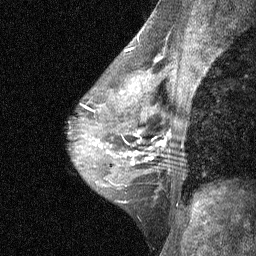
Breast MRI (dynamic contrast-enhanced), one sagittal slice. Slice 39 of 64 in the series (ordered by position). Dynamic contrast-enhanced study with each time point stored as its own series, time point 3 of 4 at this slice position (ordered by acquisition time). 1.5 T. TE 4.8 ms, TR 27 ms. 2 mm slice thickness. 256 × 256 image matrix, field of view 180 × 180 mm. Female patient, age 44 years. From the clinical record (not read from this slice): setting: breast cancer imaged before/during neoadjuvant chemotherapy; receptor status: HR-positive, HER2-negative.
Outlined on this slice (semi-automatic segmentation, software-assisted and operator-edited):
- analysis volume of interest (the breast-tissue region the enhancement analysis was run in; not a lesion): bounding box (x1, y1, x2, y2) in pixels: (115, 117, 185, 188)
- tumour enhancement mask (voxels above the 90 % enhancement threshold inside the analysis volume of interest): (133, 135, 166, 159)